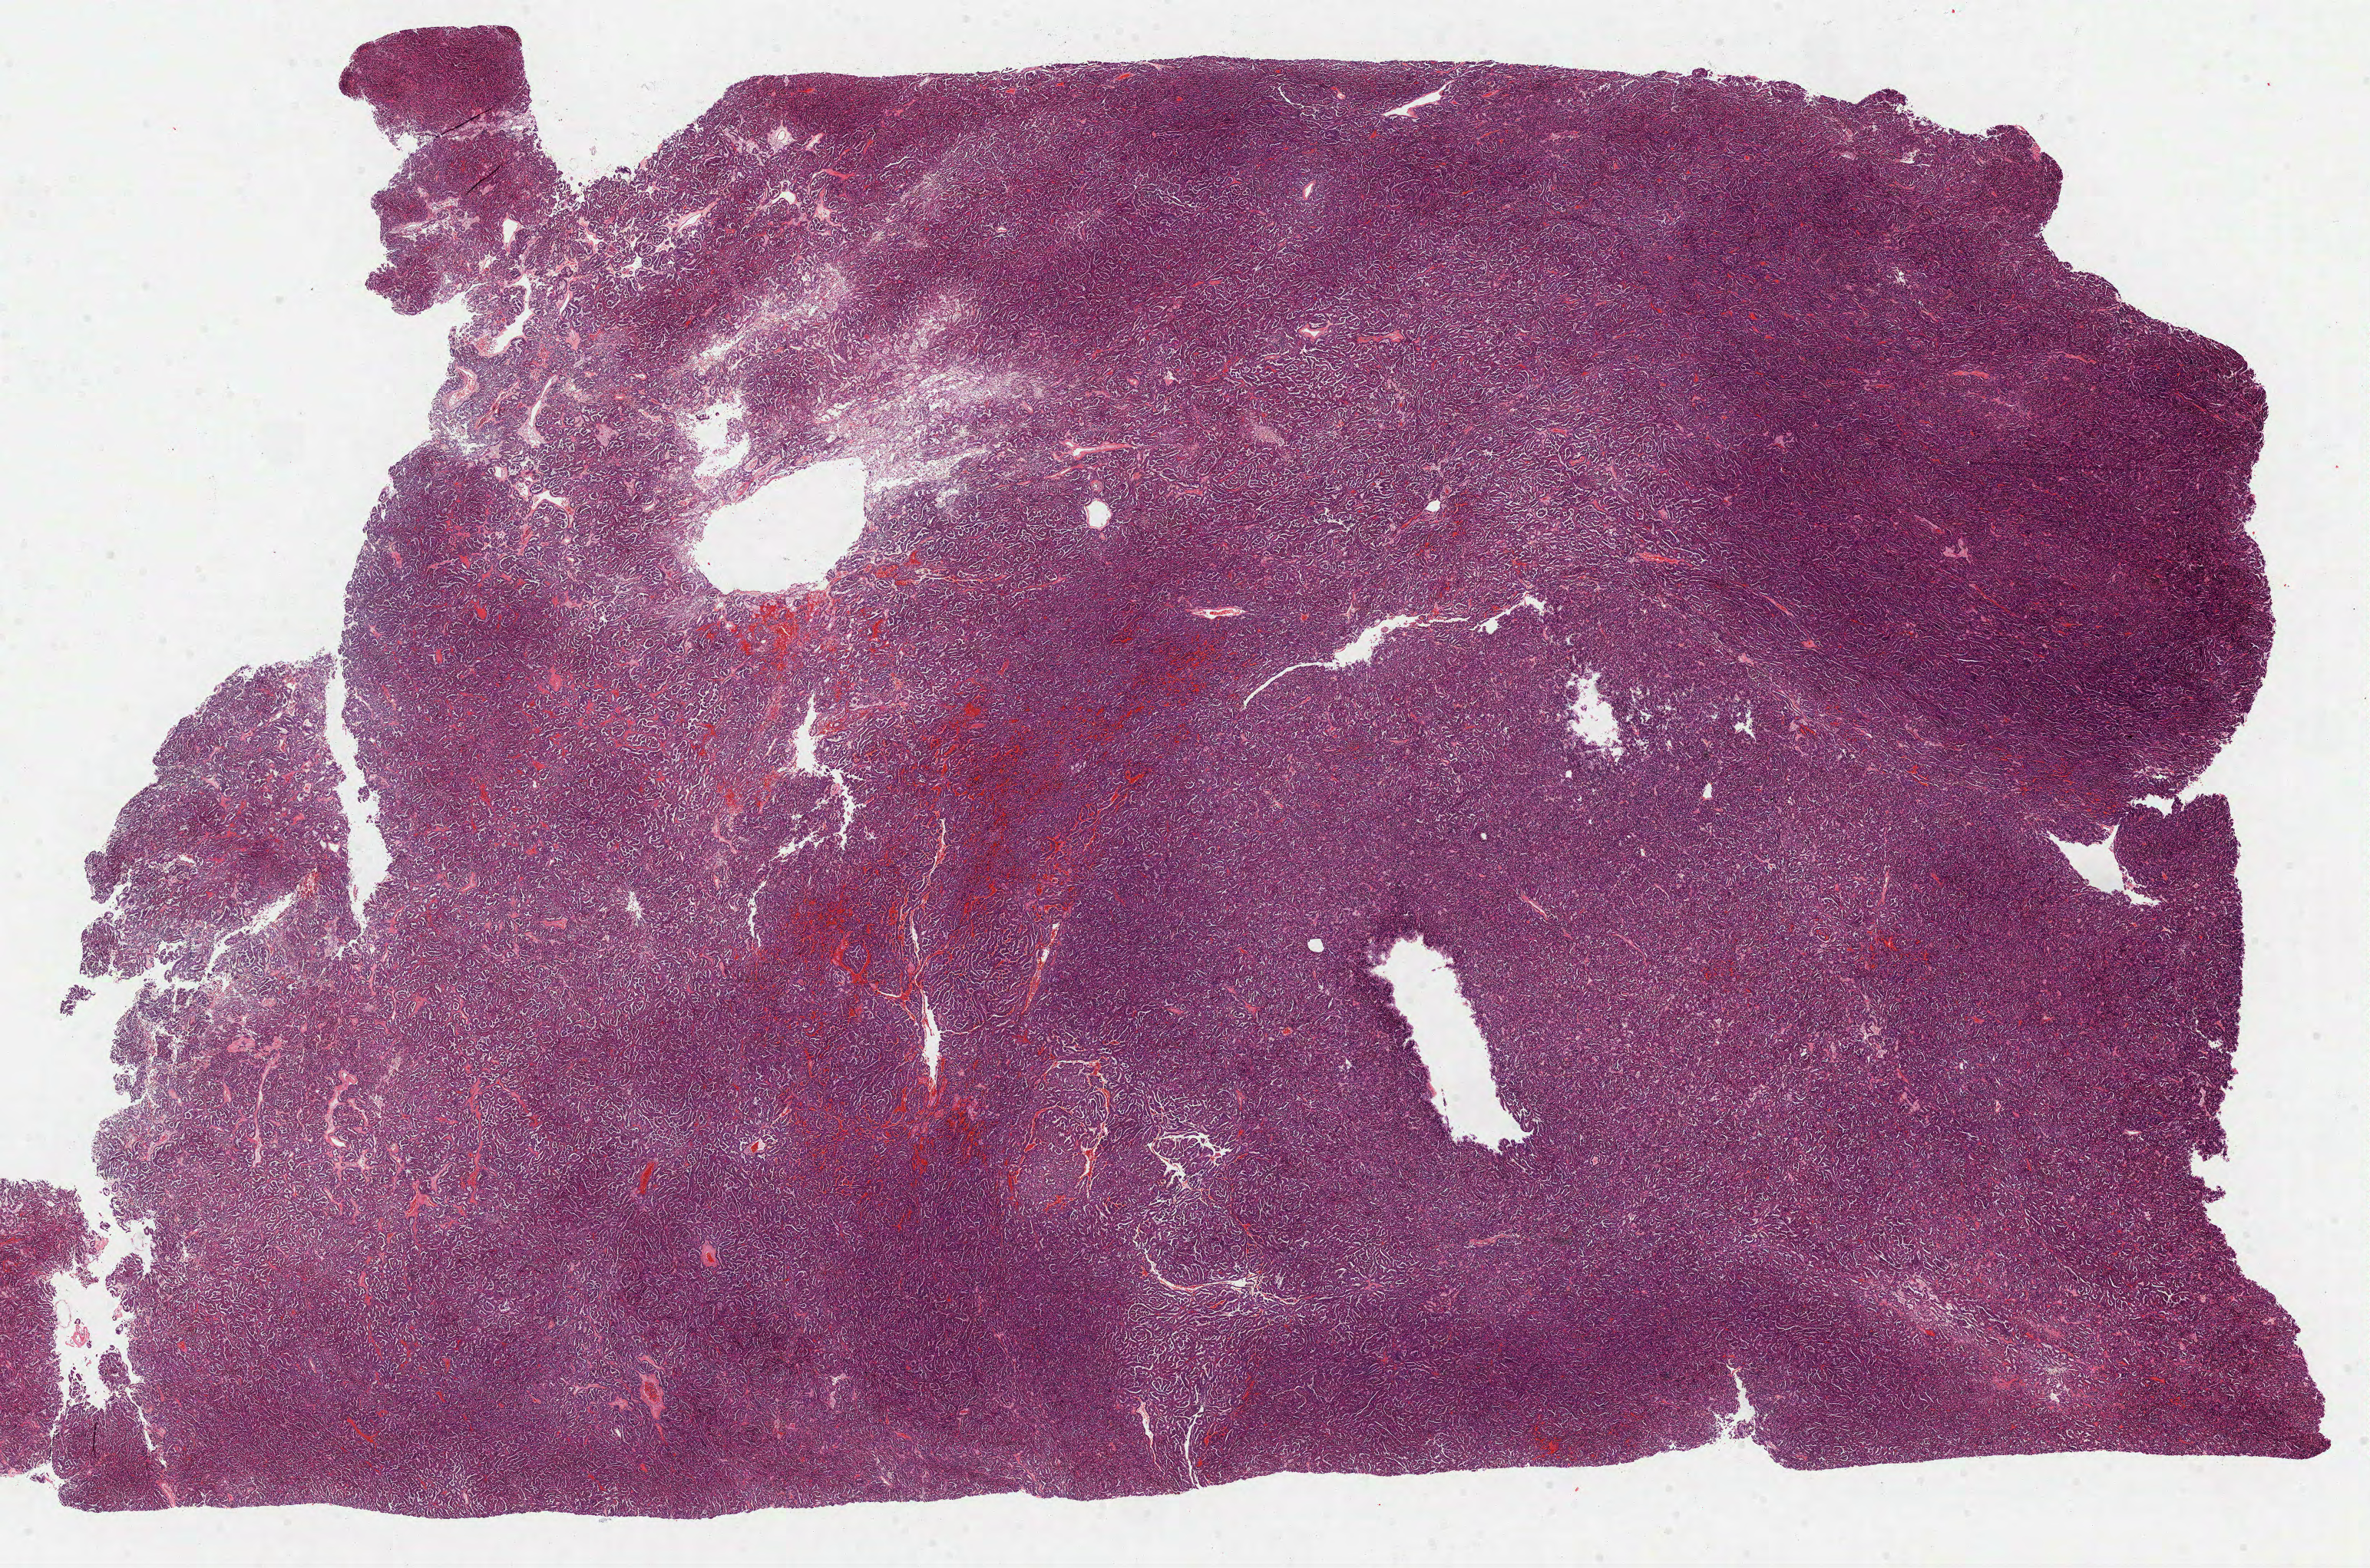
H&E whole-slide image, whole scanned area (about 24.9 x 16.5 mm) shown as a low-resolution overview; formalin-fixed paraffin-embedded (FFPE) diagnostic section; kidney, primary tumour sample. Patient: male, age at initial diagnosis 59 years.
TNM: T2 N0 M0. AJCC pathologic stage: II (7th edition). Pathologic diagnosis: Papillary adenocarcinoma, NOS.